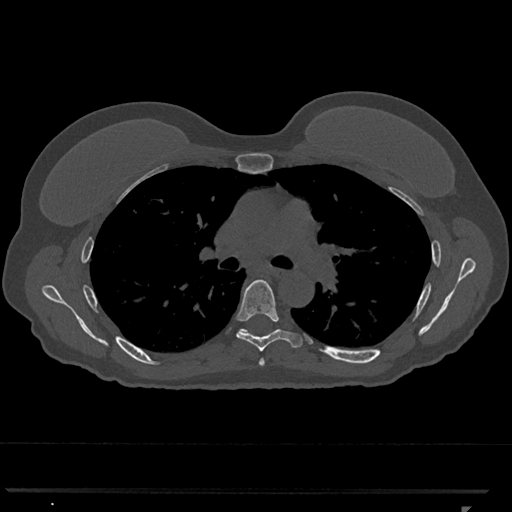
CT including the spine, one axial slice; slice 759 of 793 in the series (ordered by position); 120 kVp; bone window (W 1800 / L 400 HU); 512 × 512 image matrix, field of view 380 × 380 mm. Patient: female, 62 years. From the clinical record (not read from this slice): primary cancer: renal.
Outlined on this slice (semi-automatic segmentation, software-assisted and operator-edited):
- T5 vertebra: bounding box <259,359,265,366> (left, top, right, bottom; pixels)
- T6 vertebra: <236,279,302,351>